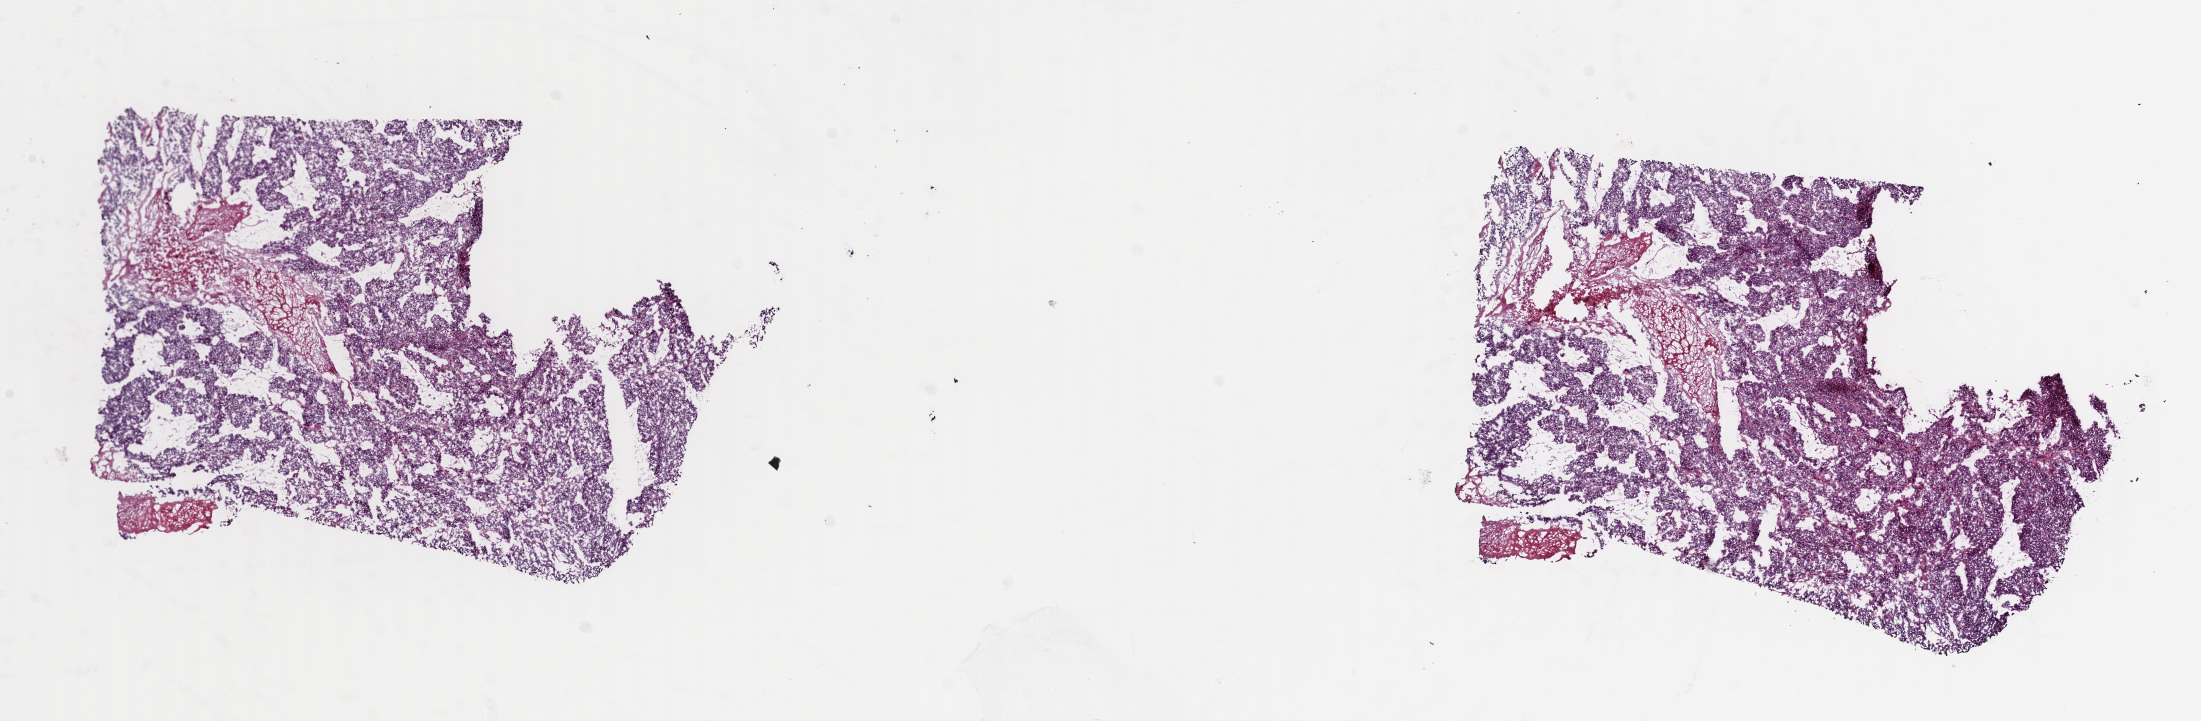
Whole-slide histology image, Hematoxylin and eosin (H&E) stained, low-resolution overview of the scanned area, about 17.4 x 5.7 mm (slide scanned at 40x); frozen section; sample: primary tumour, adrenal cortex. Female, age 59 years at initial diagnosis. Slide review estimates, as recorded: tumour cells 90%, tumour nuclei 90%, normal cells 0%, stromal cells 5%, necrosis 5%. Inflammatory infiltration, as recorded: lymphocyte infiltration 0%, monocyte infiltration 0%, neutrophil infiltration 0%.
* lymph nodes positive (case pathology): 0 of 20 examined
* pathologic diagnosis: Adrenal cortical carcinoma (cortex of adrenal gland)
* laterality: left